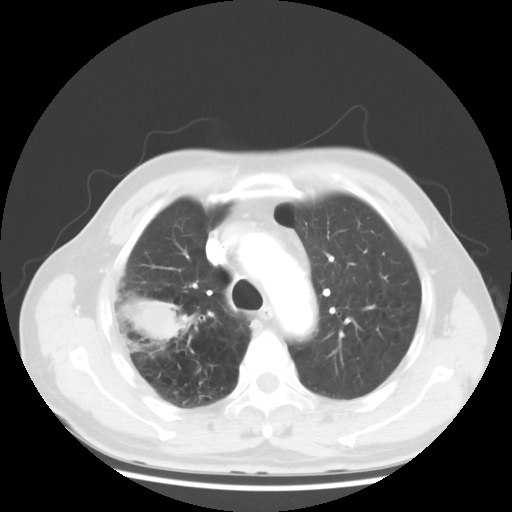
Chest CT, one axial slice. Slice 37 of 50 in the series (ordered by position). Reconstruction kernel STANDARD. 120 kVp. Lung window (W 1500 / L -600 HU). 5 mm slice thickness. 512 × 512 image matrix, field of view 360 × 360 mm. Patient: male, 69 years. Case-level facts recorded for this patient, not image findings: clinical TNM (as recorded): T3 N0 M0; histopathological grade: G3.
Annotated regions visible in this slice (bounding box drawn by a radiologist):
- lung tumour (recorded histology: adenocarcinoma): box from (x=115, y=289) to (x=202, y=356) px